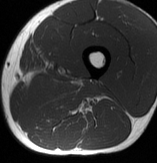
MRI of an extremity soft-tissue mass, one axial slice; slice 25 of 70 in the series (ordered by position); MR volume resampled by the dataset authors to the PET/CT grid (not the native acquisition matrix); 3.27 mm slice thickness; 157 × 163 image matrix, field of view 153 × 159 mm. Male patient. From the clinical record (not read from this slice): histological type: extraskeletal osteosarcoma; grade: high; site of the primary tumour: left adductur.
Annotated regions visible in this slice (expert contour drawn on MRI and transferred to this co-registered scan by the dataset authors):
- gross tumour volume (mass): bounding box [x1, y1, x2, y2] px = [26, 76, 103, 109]